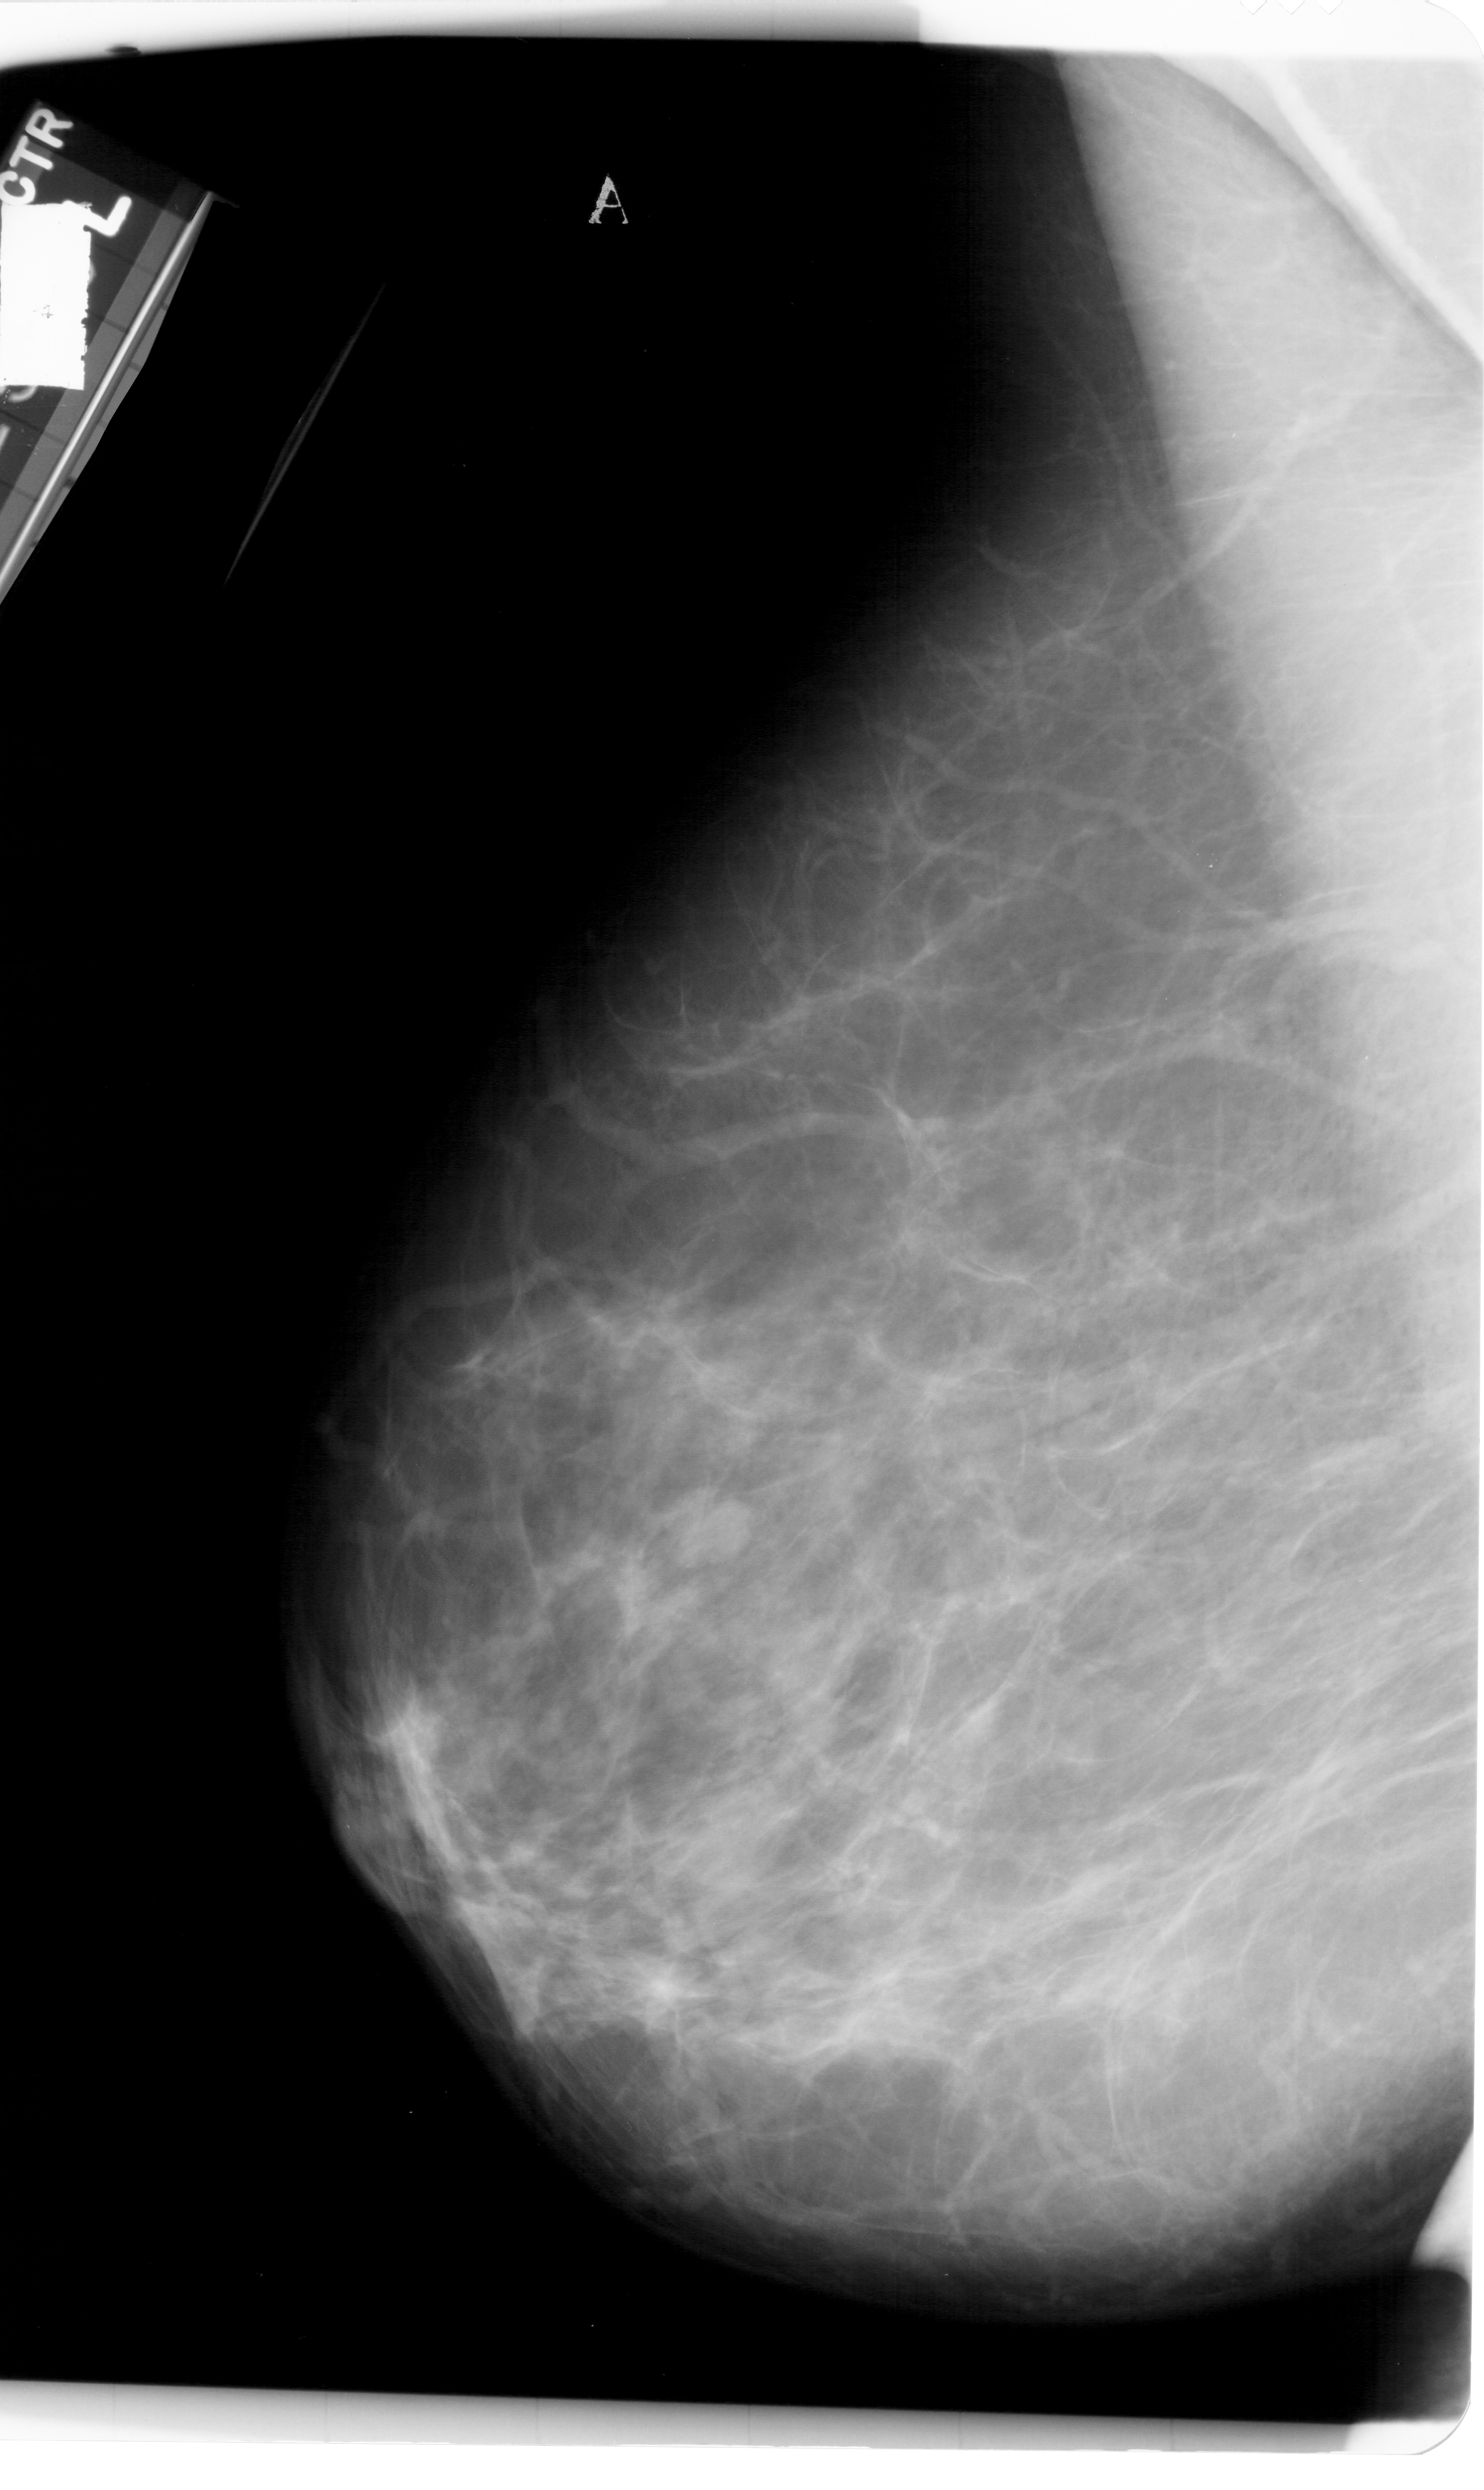
Digitized screen-film mammogram; left breast; mediolateral oblique (MLO) view; breast composition: scattered fibroglandular densities (BI-RADS density category 2 of 4).
Mass, shape lobulated, margins circumscribed; BI-RADS assessment category 4; pathology (as recorded): benign.